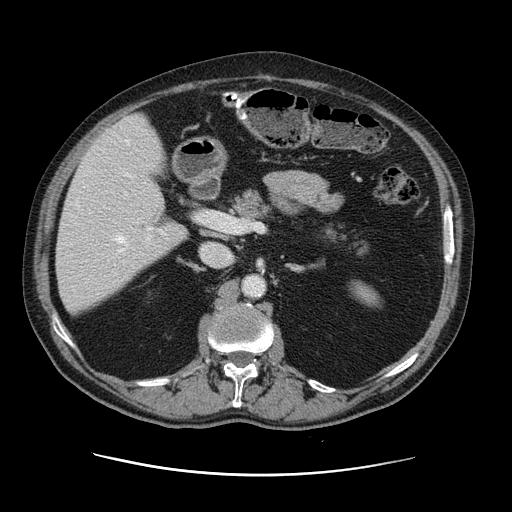
Contrast-enhanced abdominal CT, one axial slice. Position 67 of 141 along the scan axis. Soft-tissue window (W 400 / L 40 HU). 512 × 512 image matrix, field of view 395 × 395 mm. Male patient, age 72 years. From the clinical record (not read from this slice): diagnosis: colorectal cancer liver metastases, imaged before liver resection; multiple liver metastases: yes; largest metastasis: 5.4 cm; disease in both lobes: yes.
Structures marked on this image (manually delineated by an expert):
- hepatic veins: box from (x=115, y=140) to (x=145, y=252) px
- liver: (x=57, y=116)–(x=186, y=315)
- planned liver remnant (the part of the liver to remain after resection): (x=56, y=187)–(x=186, y=314)
- portal vein (with intrahepatic branches): (x=137, y=214)–(x=203, y=240)